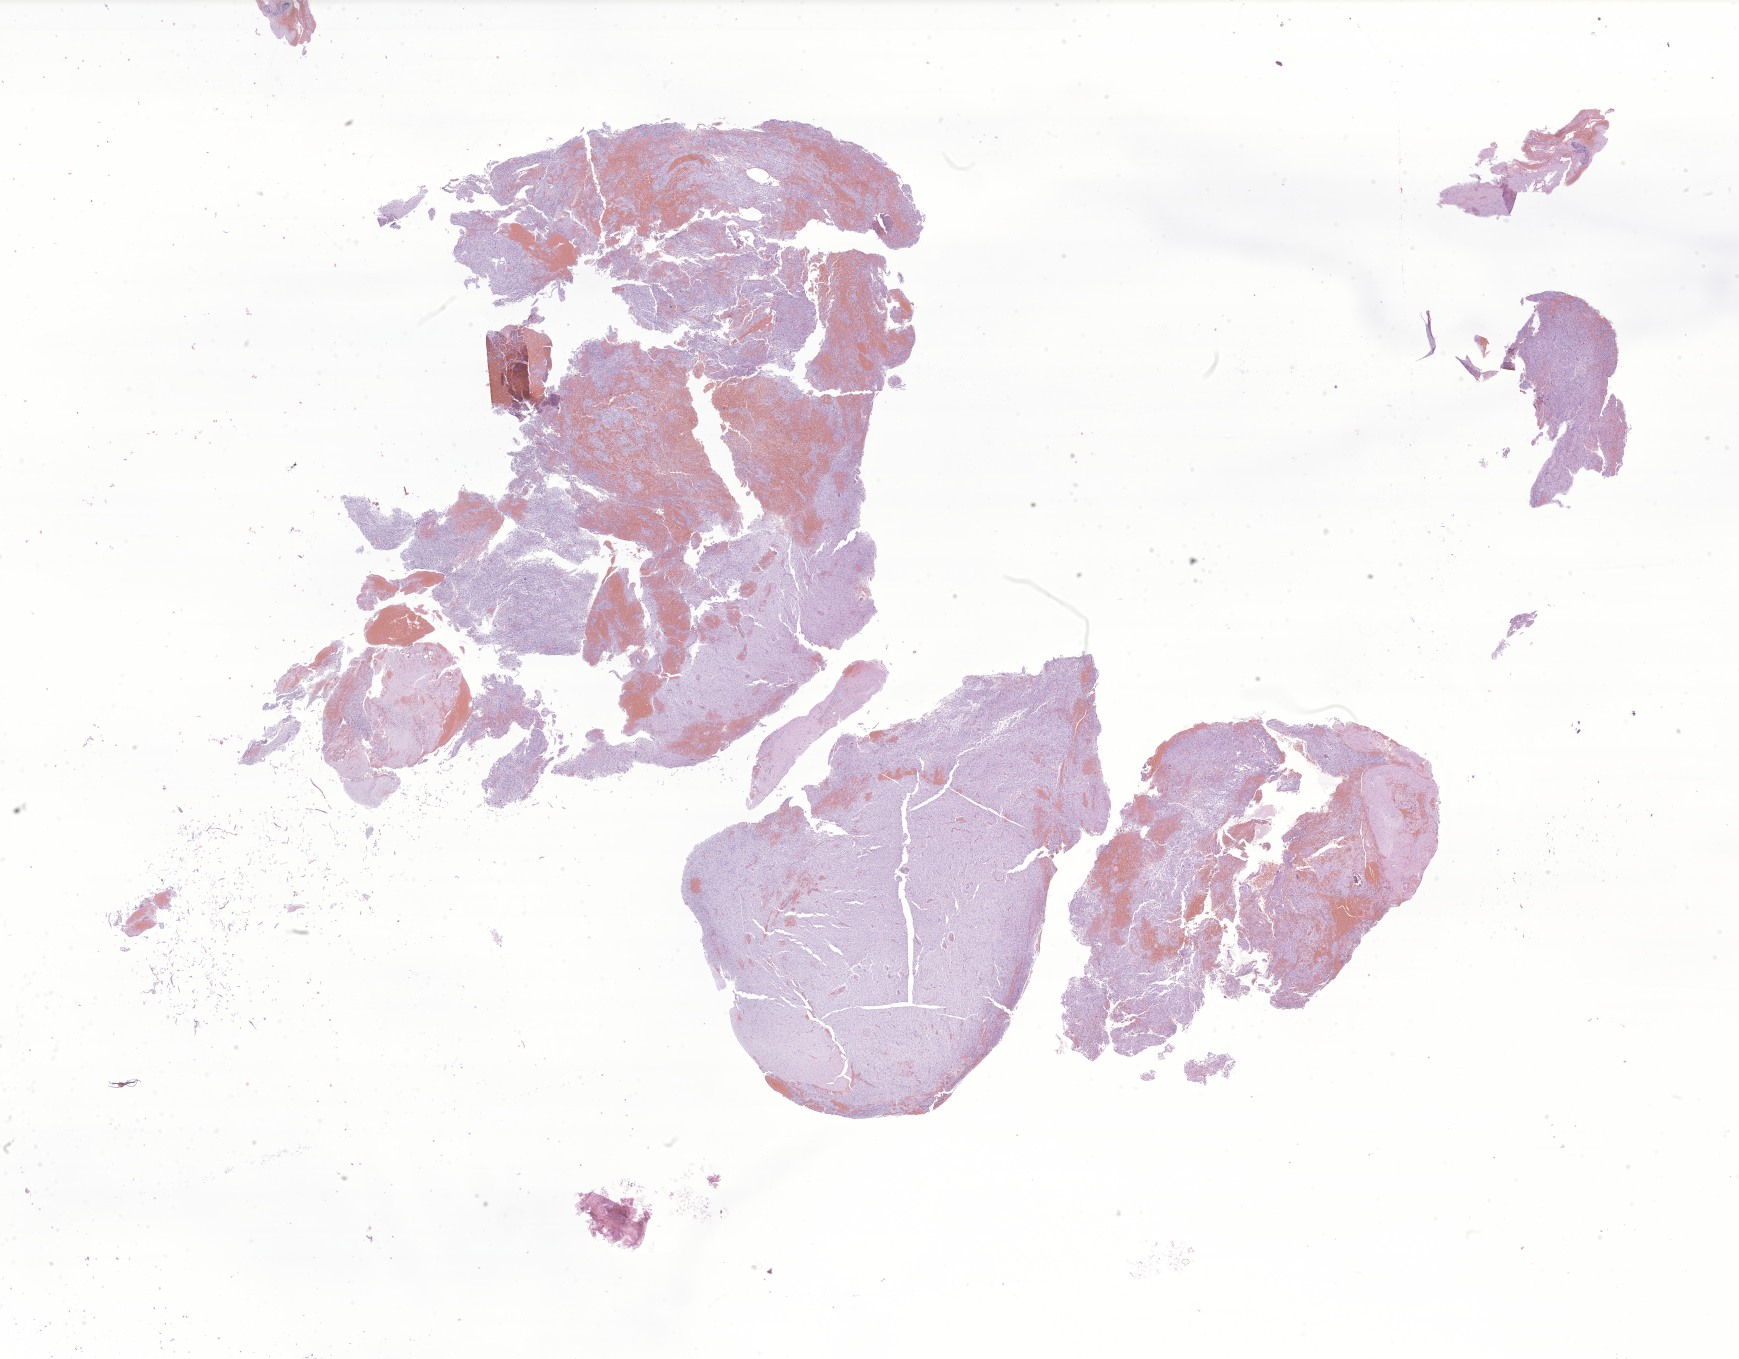
Whole-slide image, hematoxylin and eosin (H&E) stain of tumor tissue from the cerebellum, a low-resolution overview of the entire scanned area, about 29.3 x 22.9 mm. FFPE section. Patient female; age 169 months.
Recorded diagnosis: Neoplasm, malignant, uncertain whether primary or metastatic.